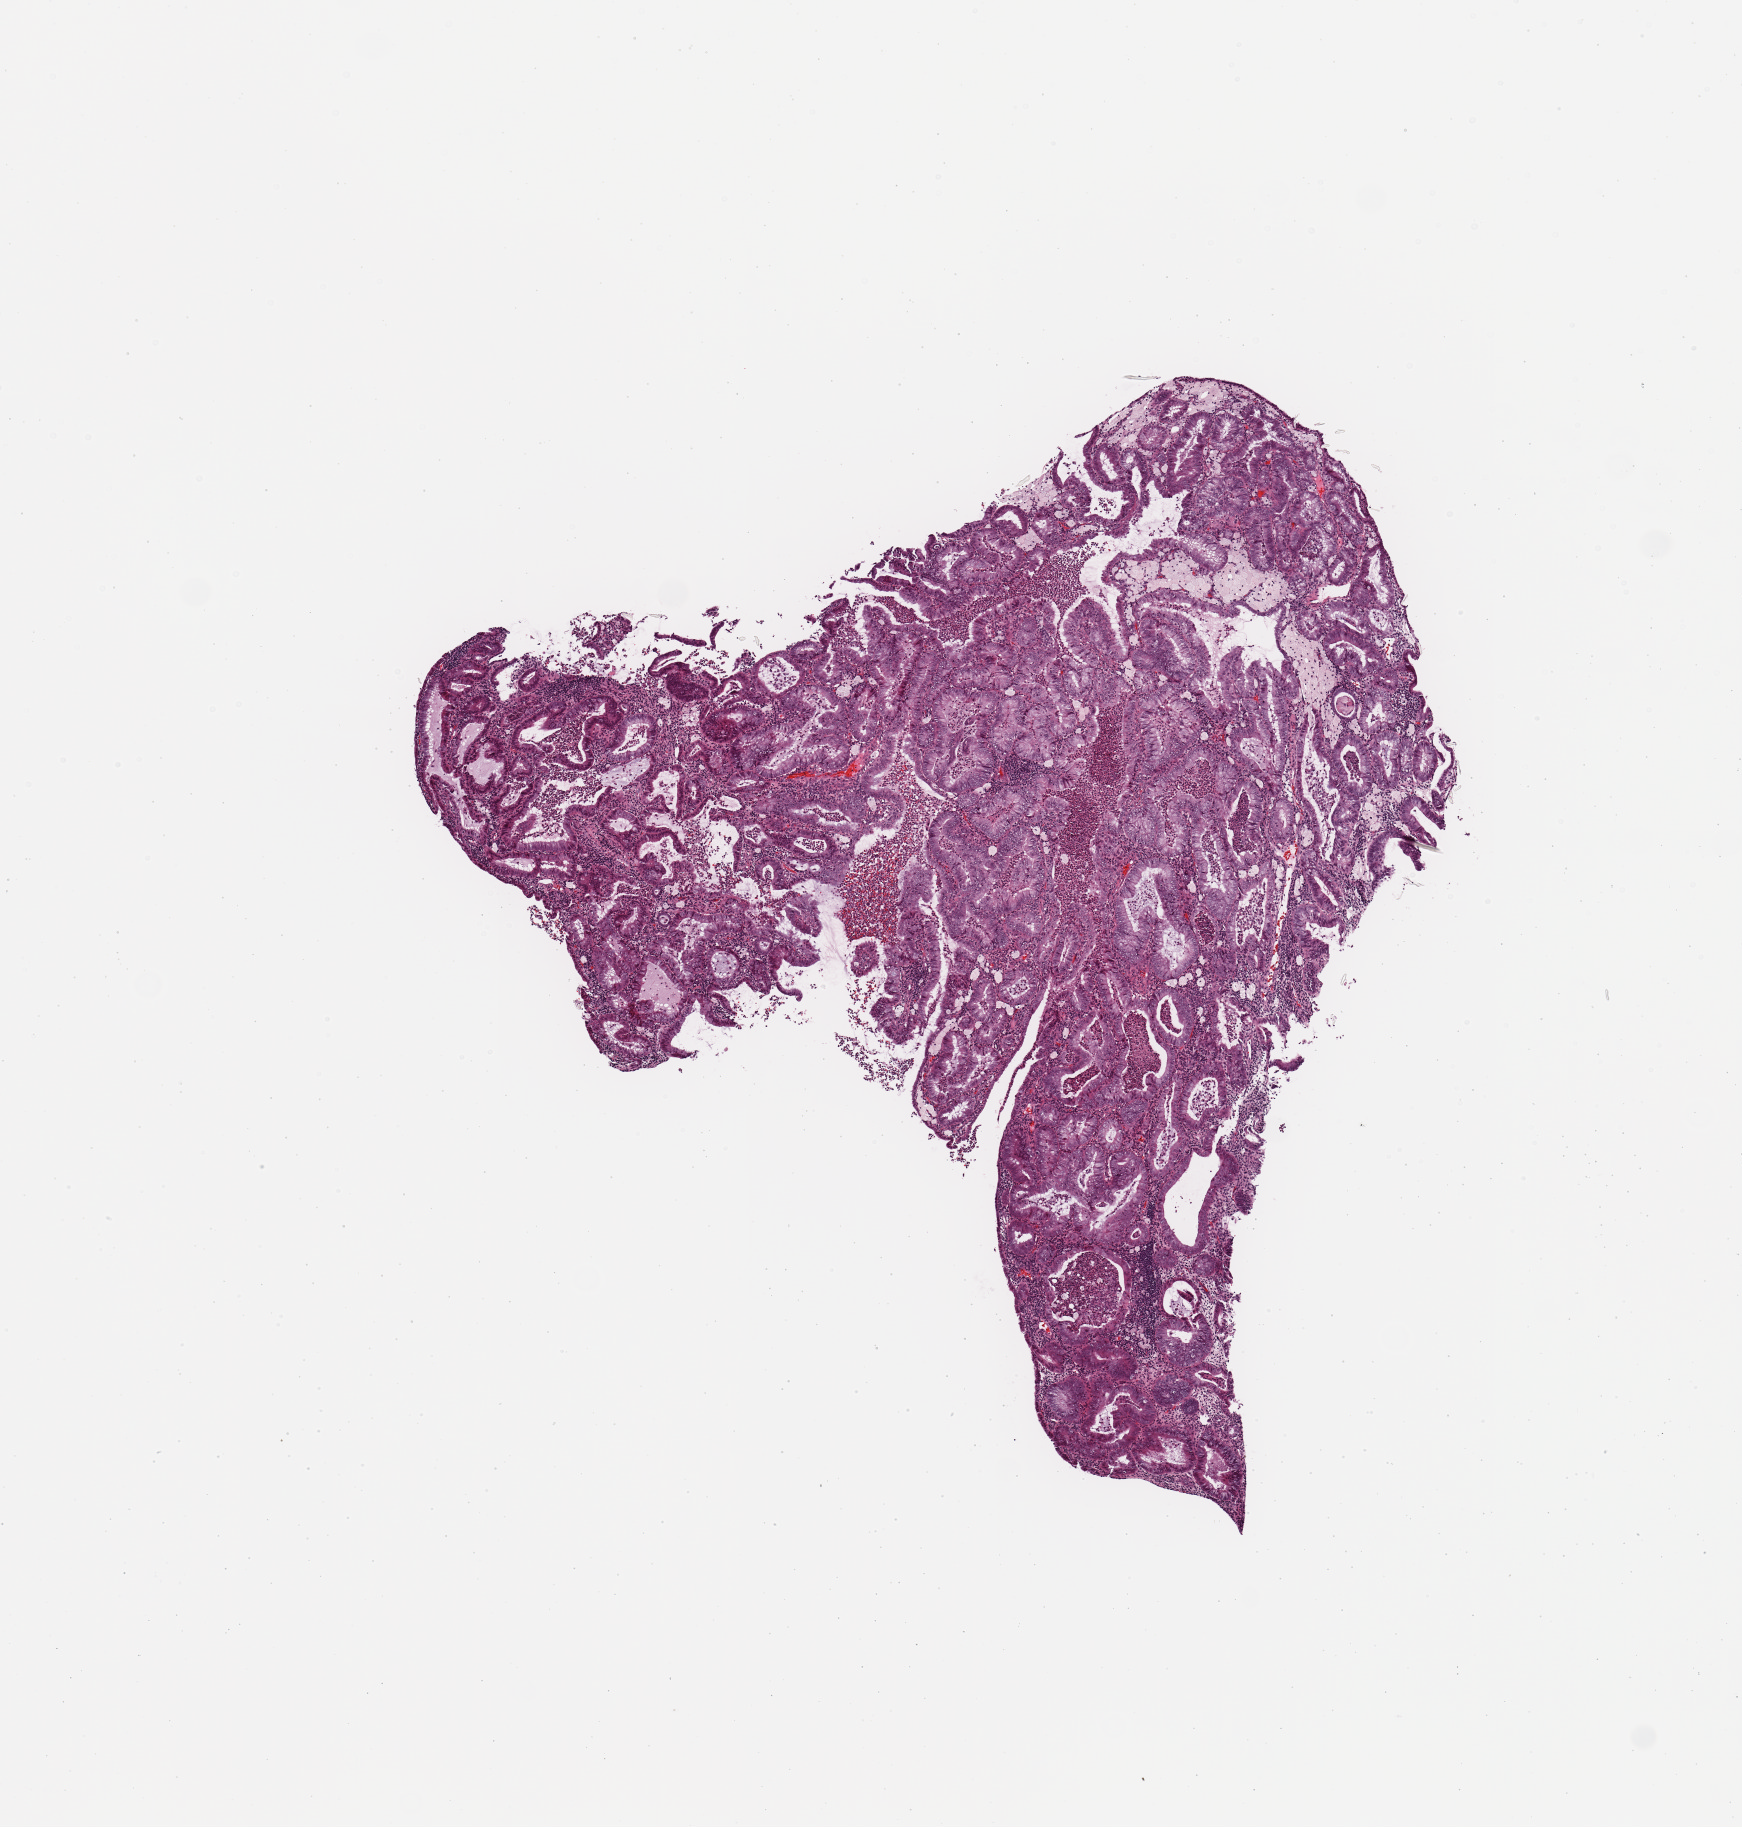
Whole-slide histology image, Hematoxylin and eosin (H&E) stained, low-resolution overview of the scanned area, about 6.9 x 7.2 mm (slide scanned at 20x). Tumour tissue sample, sampled site: uterus. Patient: female, age 54 years. Histologic grade: G2 (moderately differentiated). Pathologist review of this section (percent, as recorded): tumour nuclei 90%, necrosis 2%.
* histologic diagnosis: Endometrioid adenocarcinoma, NOS
* AJCC pathologic stage: I